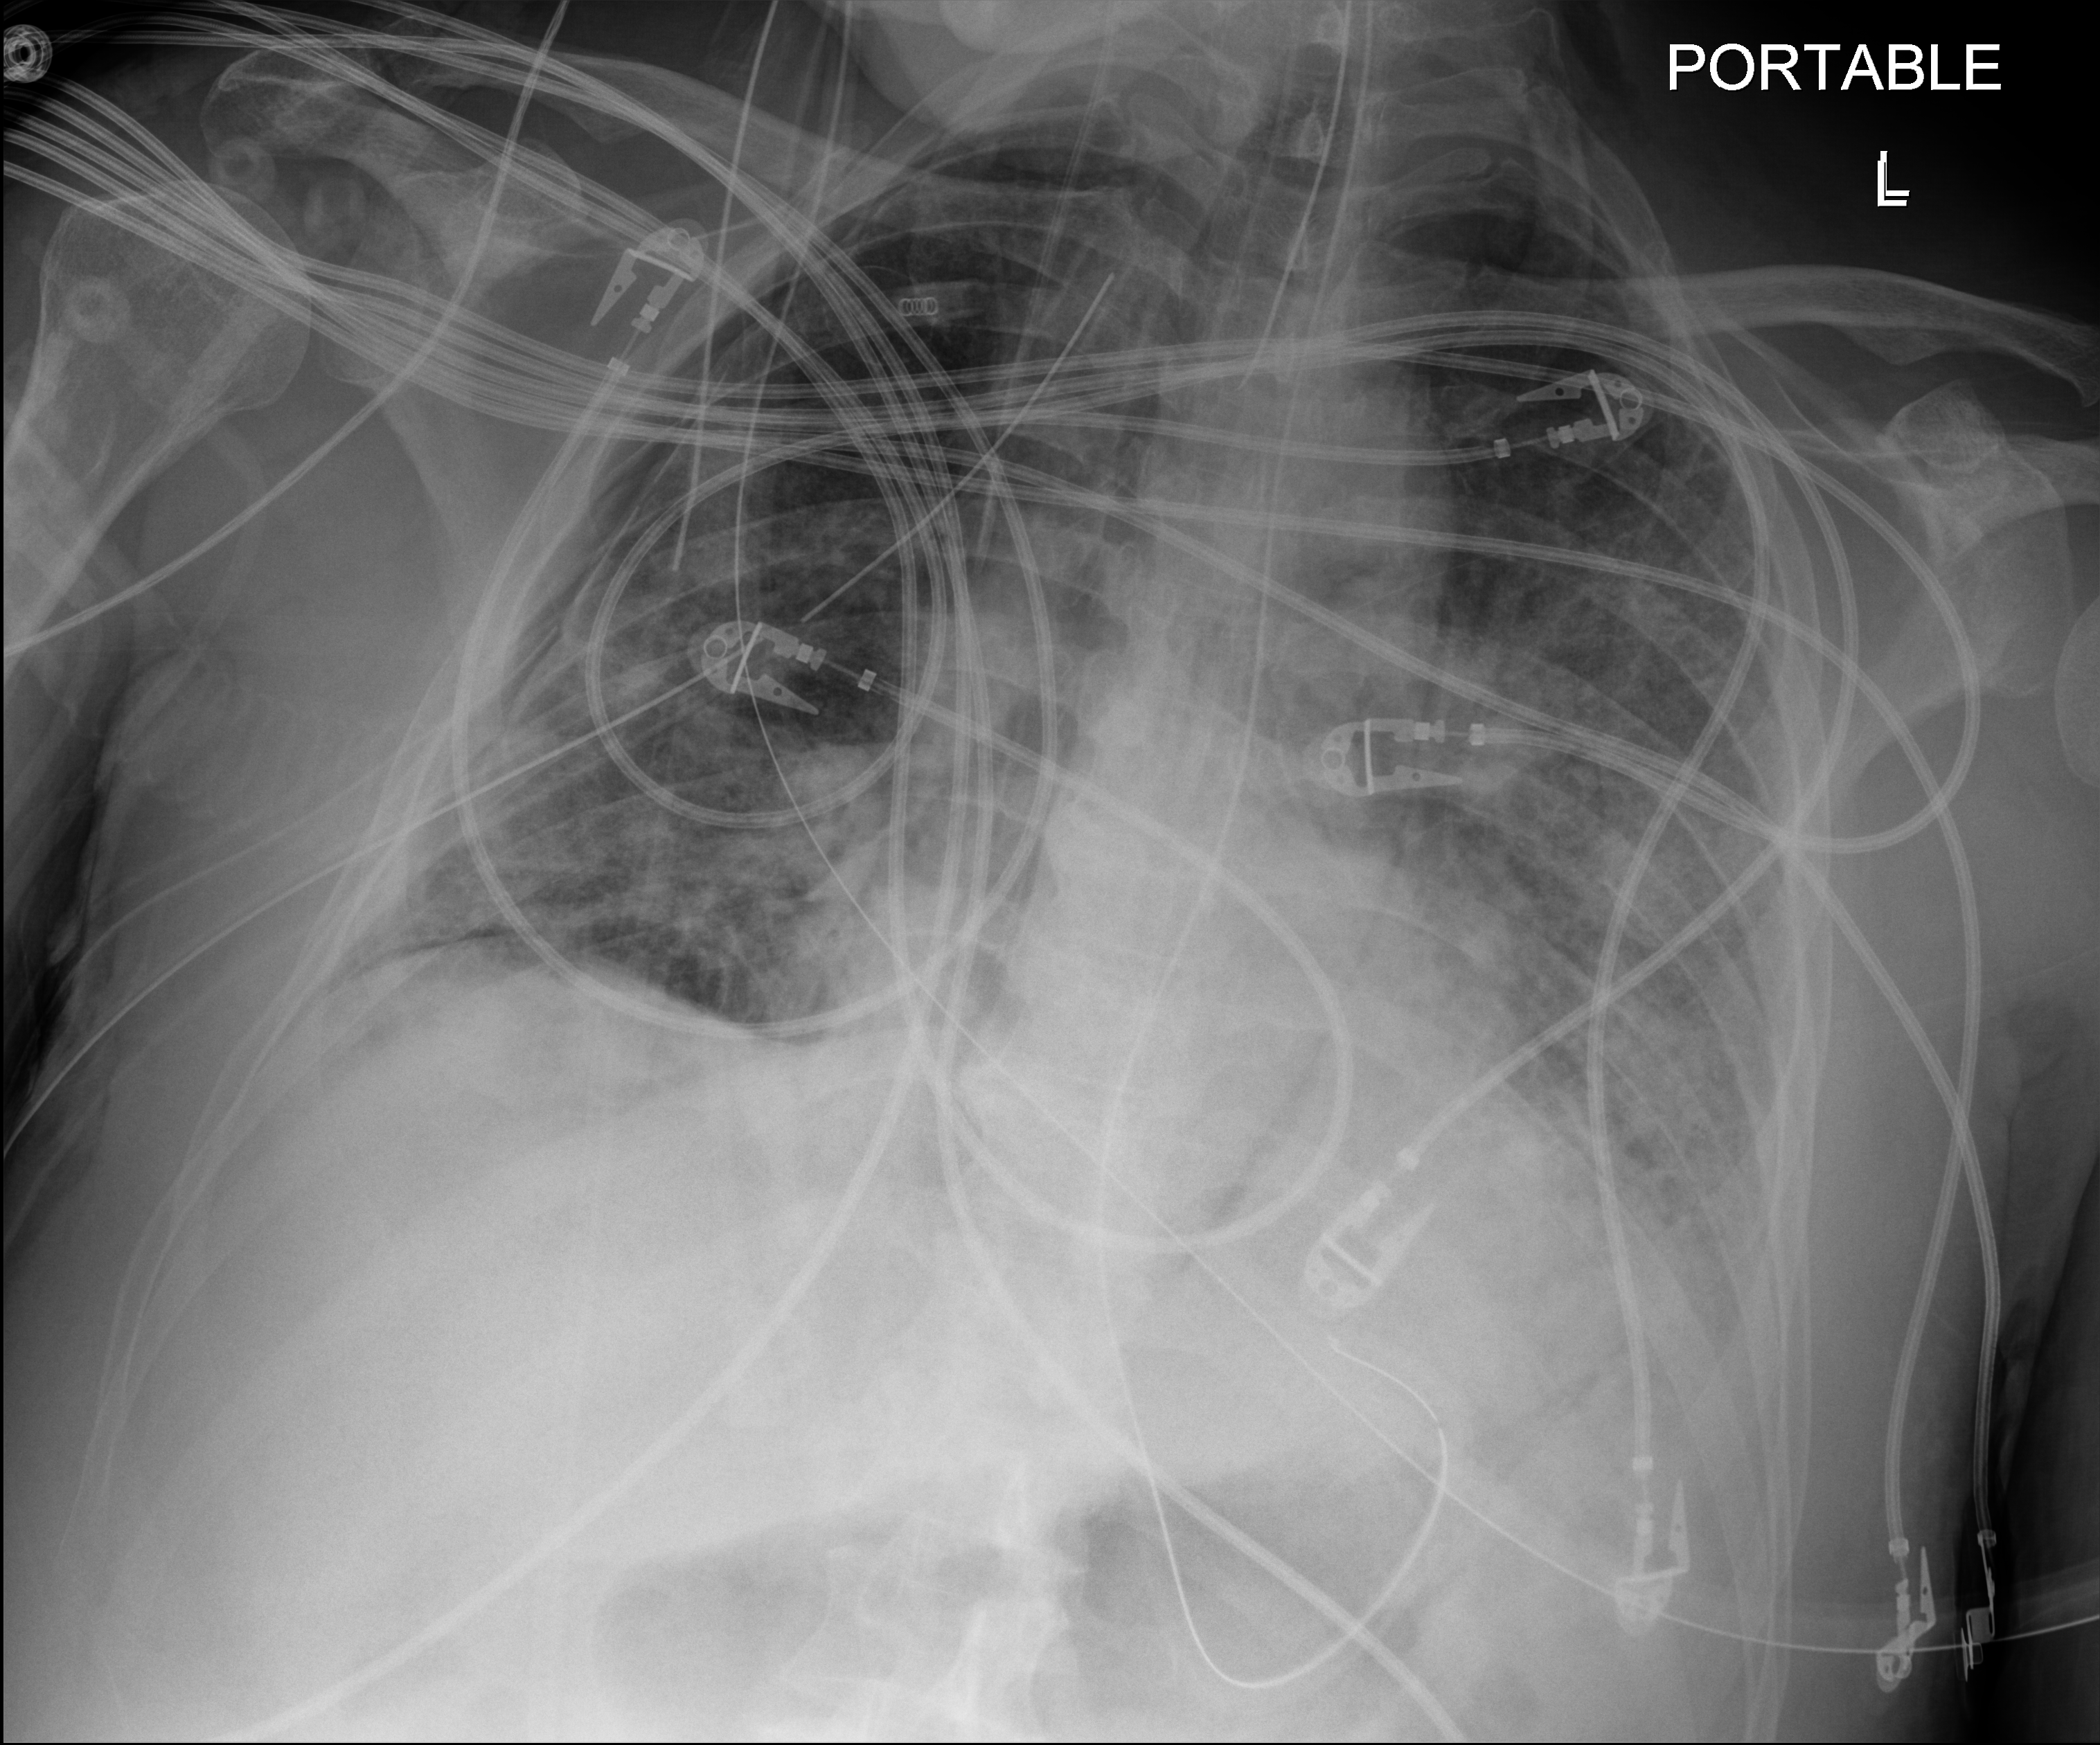
Portable chest radiograph; anteroposterior (AP) projection. Patient hospitalised with COVID-19; male, aged 60–74 years.
From the hospital-stay record, not from the radiograph (when in the stay this image was taken is not recorded): mechanically ventilated during this hospital stay: yes.